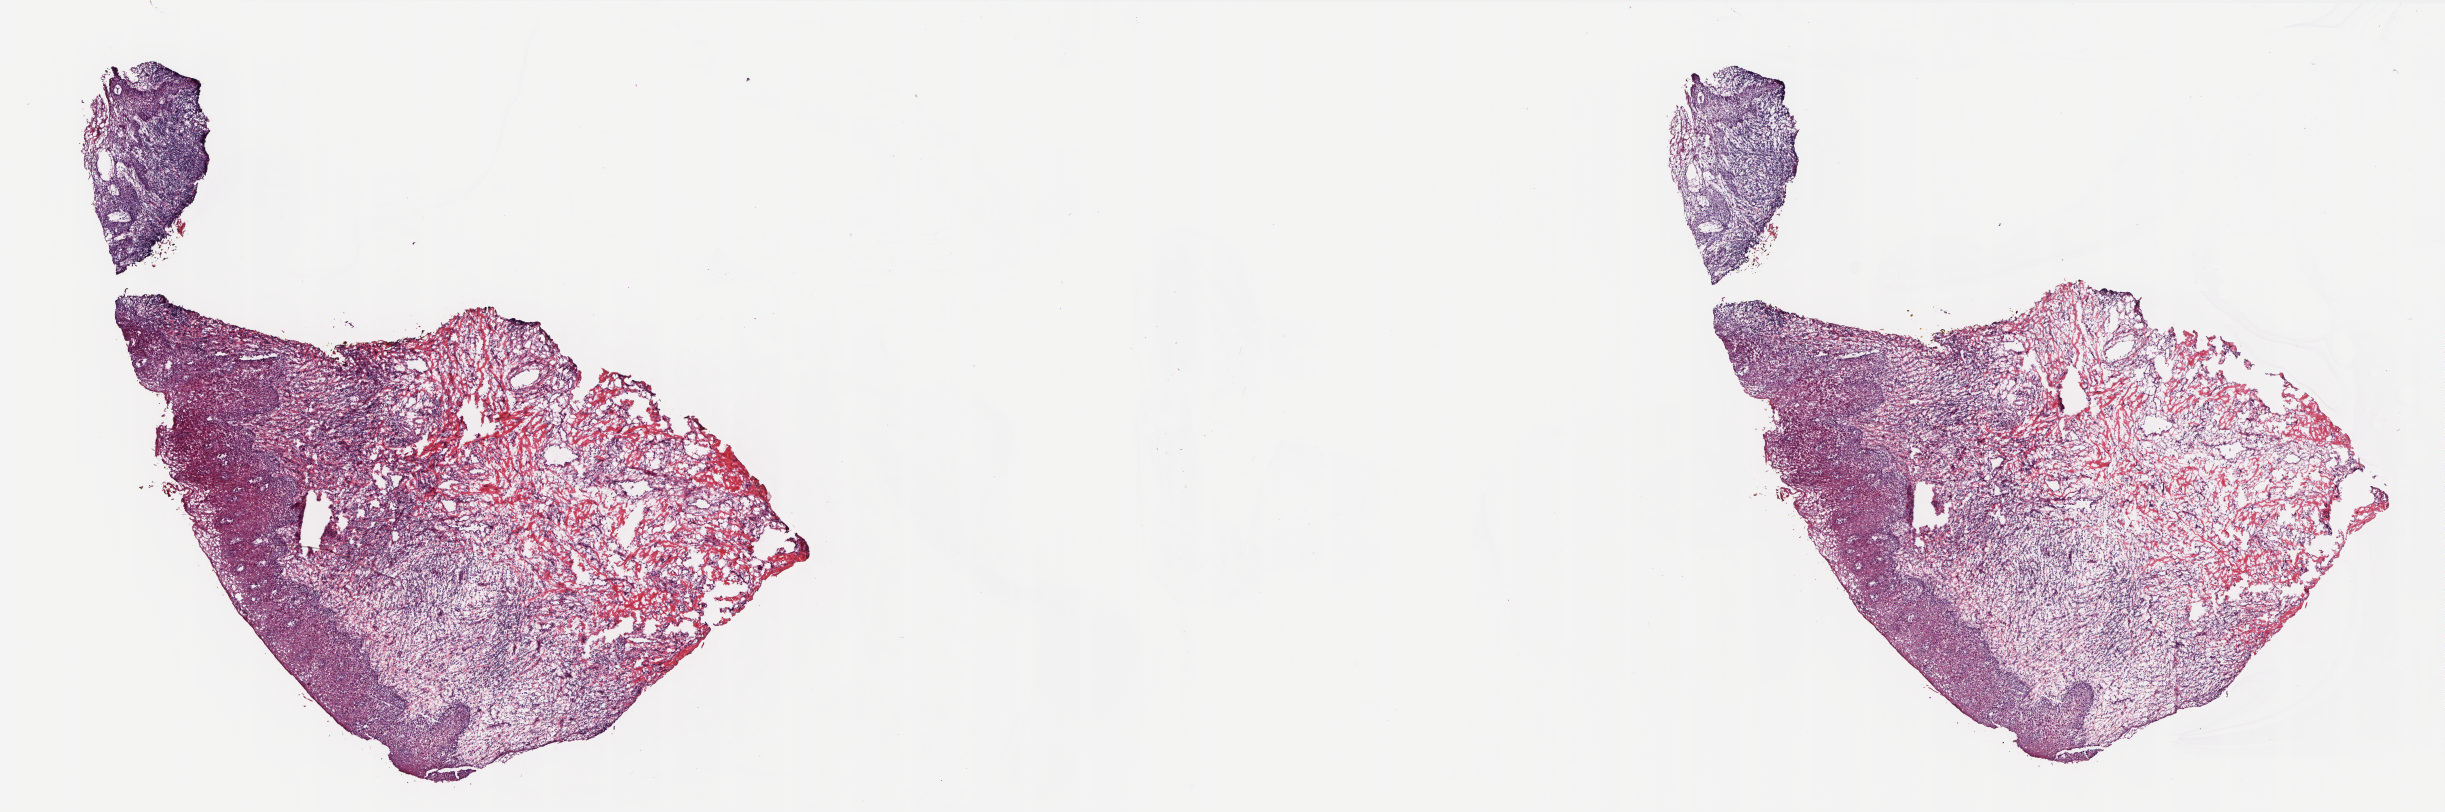
Digitized Hematoxylin and eosin (H&E) stained tissue section (whole slide), whole scanned area (about 19.7 x 6.5 mm) shown as a low-resolution overview, frozen section, solid tissue normal (non-tumour tissue) sample from the head and neck. Male, age 56 years at initial diagnosis. Pathologist review of this section (percent, as recorded): tumour cells 0%, tumour nuclei 0%, normal cells 100%, stromal cells 0%, necrosis 0%. Infiltration values recorded for this section: lymphocyte infiltration 10%, monocyte infiltration 0%, neutrophil infiltration 0%.
This section: solid tissue normal sample (biorepository sample class). Patient diagnosis: Squamous cell carcinoma, keratinizing, NOS (mouth, NOS).